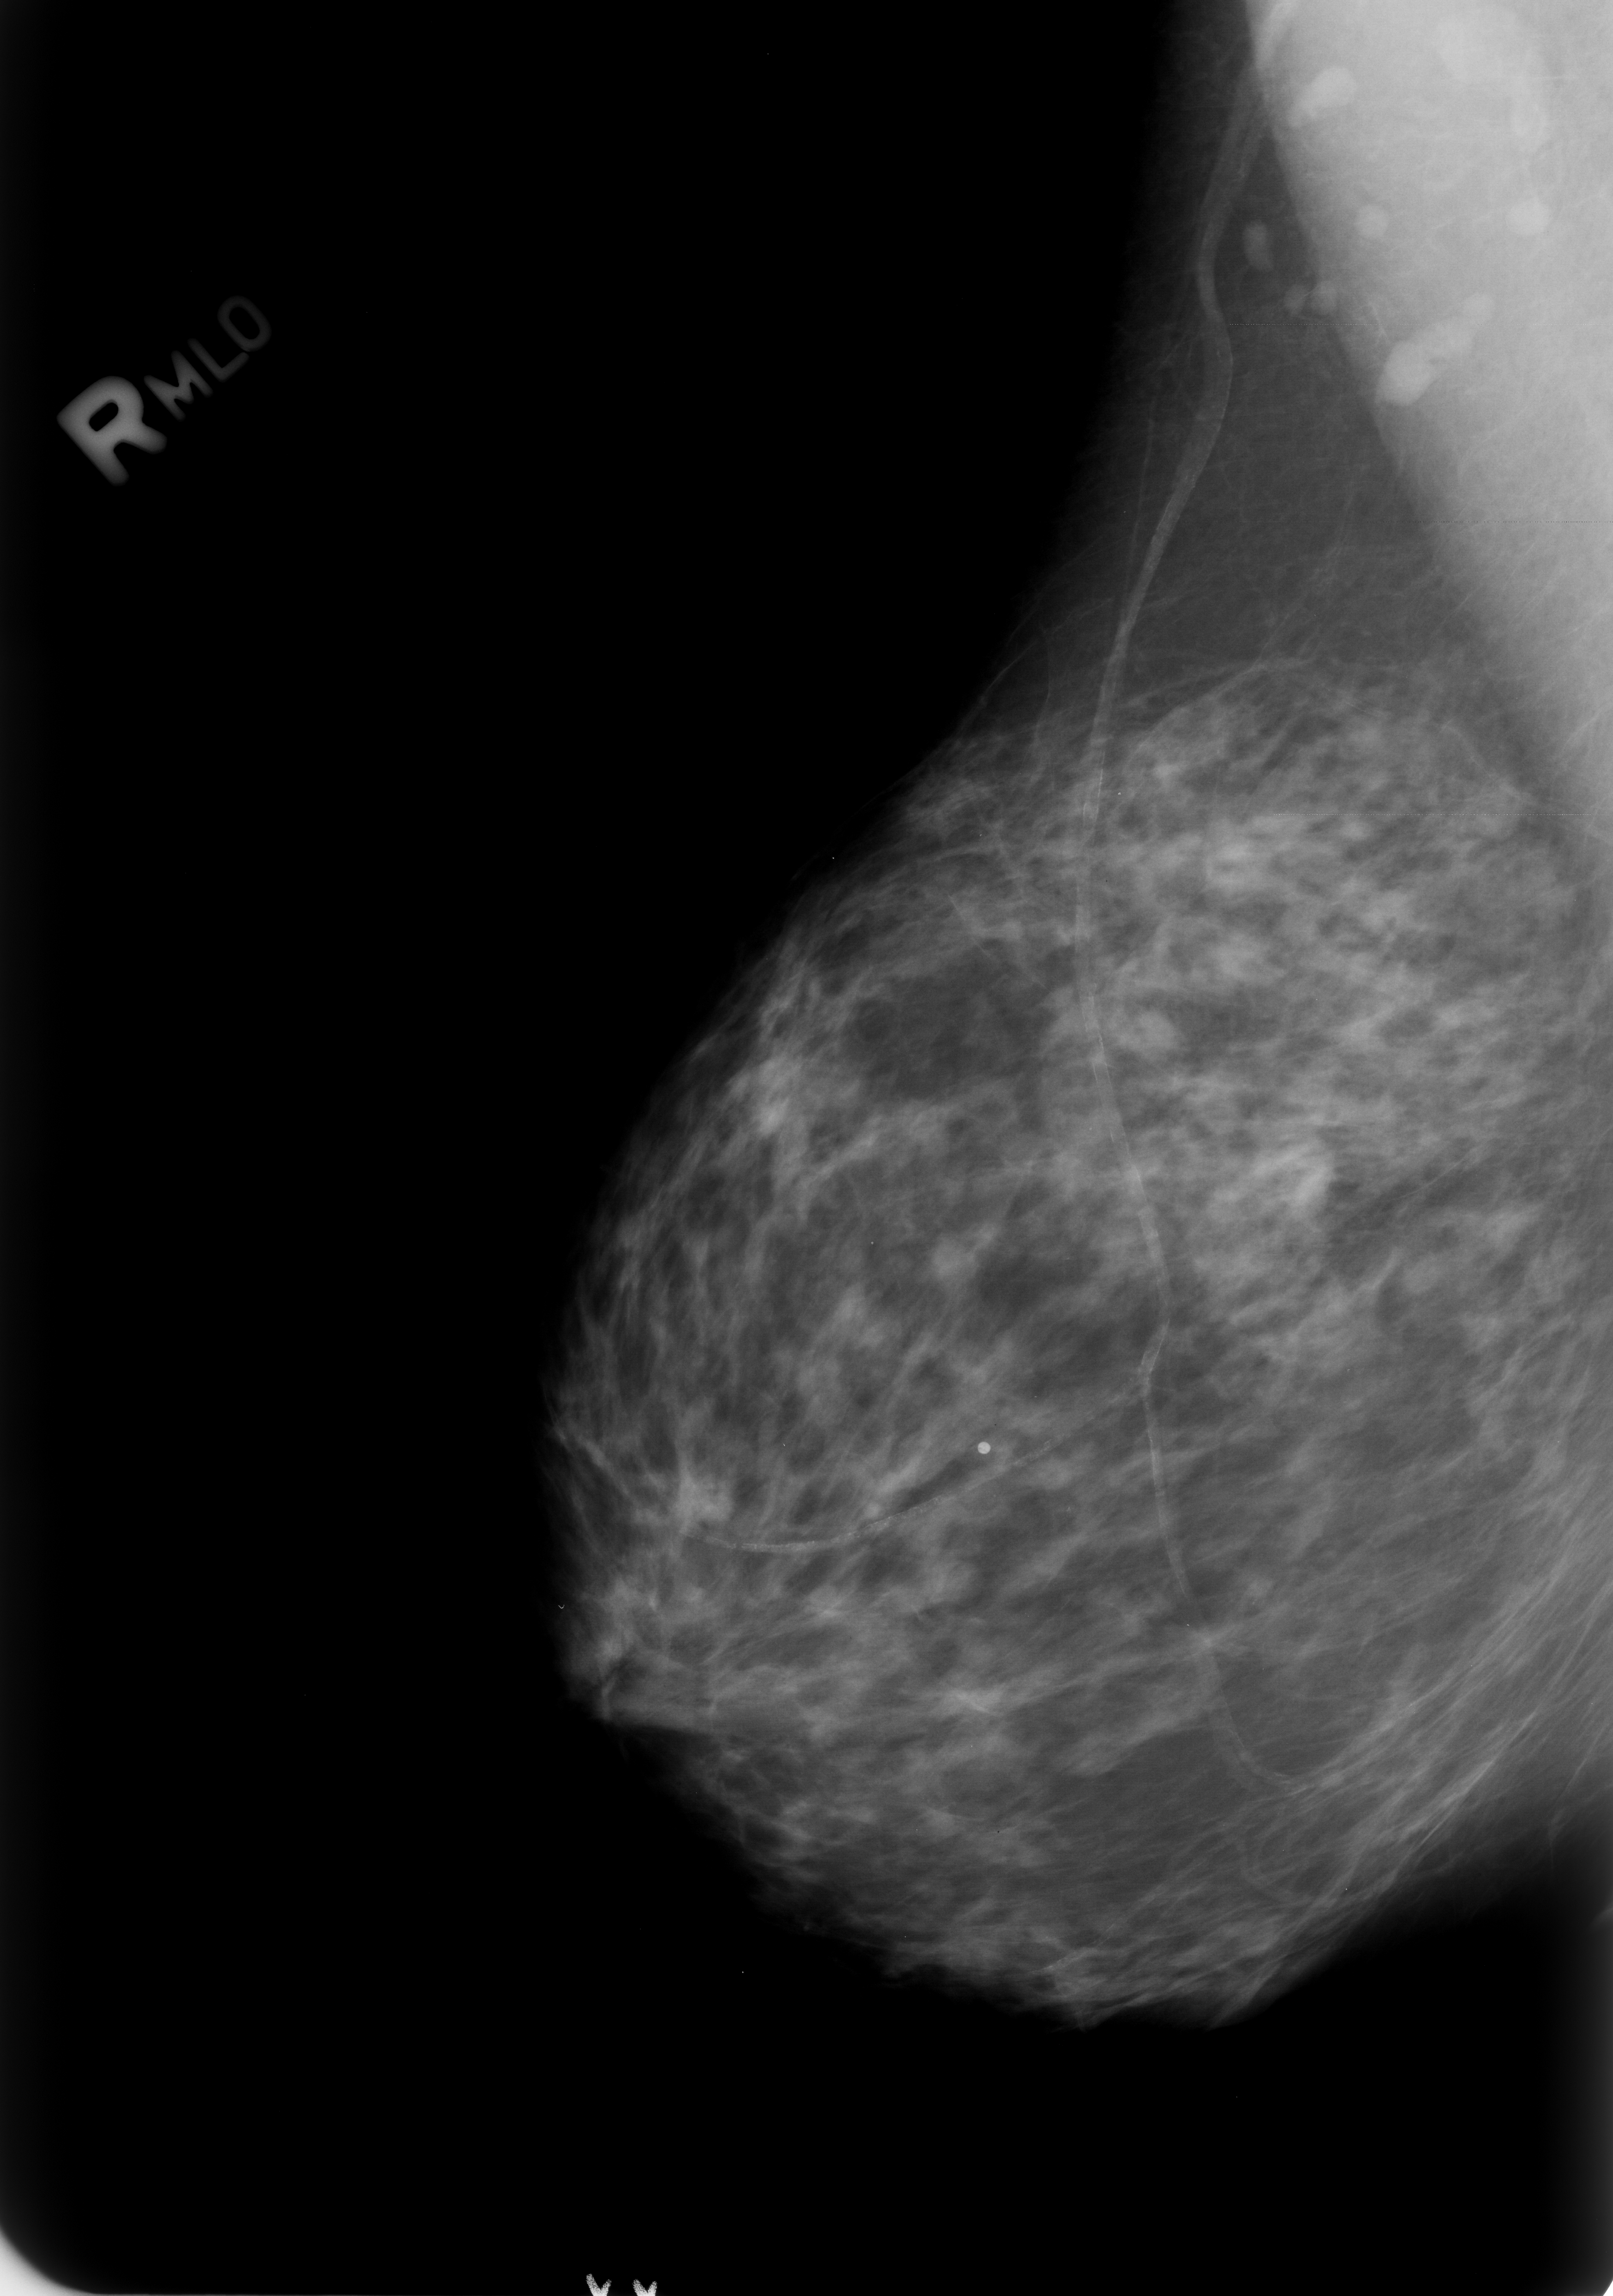
Scanned film-screen mammogram, right breast, mediolateral oblique (MLO) view, breast composition: scattered fibroglandular densities (BI-RADS density category 2 of 4).
Marked findings (only marked abnormalities are described; nothing is implied about the rest of the image): Finding 1 of 2: calcifications, morphology lucent center; BI-RADS assessment category 2; subtlety rating 4 on a 1 (subtle) to 5 (obvious) scale; benign; no additional work-up was recommended (benign without callback). Finding 2 of 2: calcifications, morphology vascular; BI-RADS assessment category 2; subtlety rating 4 on a 1 (subtle) to 5 (obvious) scale; benign; no additional work-up was recommended (benign without callback).